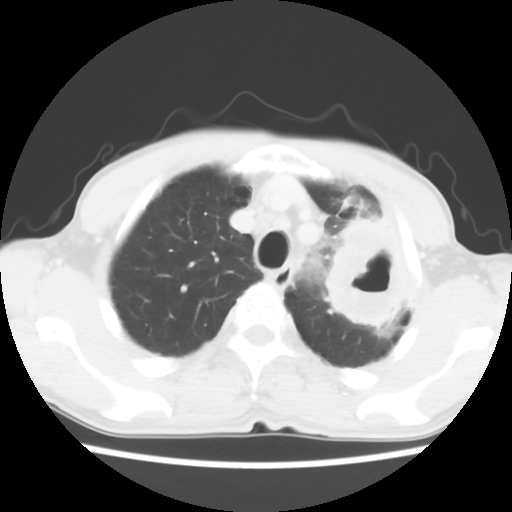
Chest CT, one axial slice. Slice 48 of 60 in the series (ordered by position). Reconstruction kernel STANDARD. Lung window (W 1500 / L -600 HU). 5 mm slice thickness. 512 × 512 image matrix, field of view 308 × 308 mm. Patient: male, 64 years. From the clinical record (not read from this slice): clinical TNM (as recorded): T3 N3 M0.
Outlined on this slice (bounding box drawn by a radiologist):
- lung tumour (recorded histology: adenocarcinoma): box from (x=319, y=205) to (x=410, y=351) px